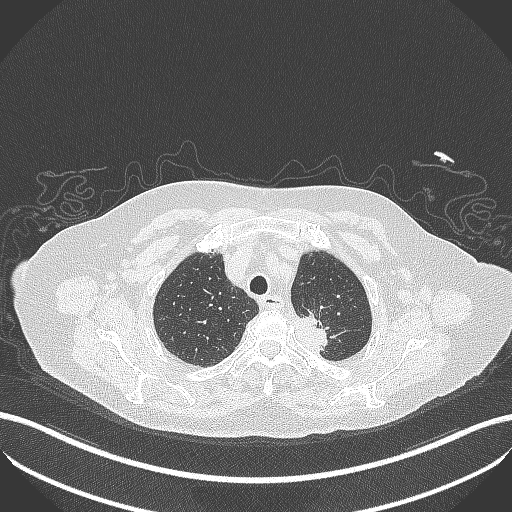
Chest CT, one axial slice; slice 285 of 353 in the series (ordered by position); 100 kVp; lung window (W 1500 / L -600 HU); 1 mm slice thickness; 512 × 512 image matrix, field of view 400 × 400 mm. Patient: female, 81 years. From the clinical record (not read from this slice): clinical TNM (as recorded): T2a N0 M0.
Annotated regions visible in this slice (rectangle marked by the reading radiologist):
- lung tumour (recorded histology: adenocarcinoma): box from (x=289, y=306) to (x=333, y=356) px